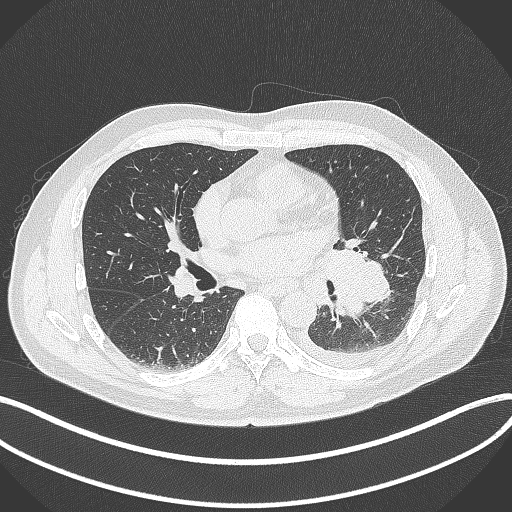
Chest CT, one axial slice. Reconstruction kernel B70f. Lung window (W 1500 / L -600 HU). 512 × 512 image matrix. Patient: male, 58 years. Case-level facts recorded for this patient, not image findings: clinical TNM (as recorded): T3 N1 M1b; histopathological grade: G3.
Outlined on this slice (bounding box drawn by a radiologist):
- lung tumour (recorded histology: small cell carcinoma): box from (x=323, y=243) to (x=395, y=325) px